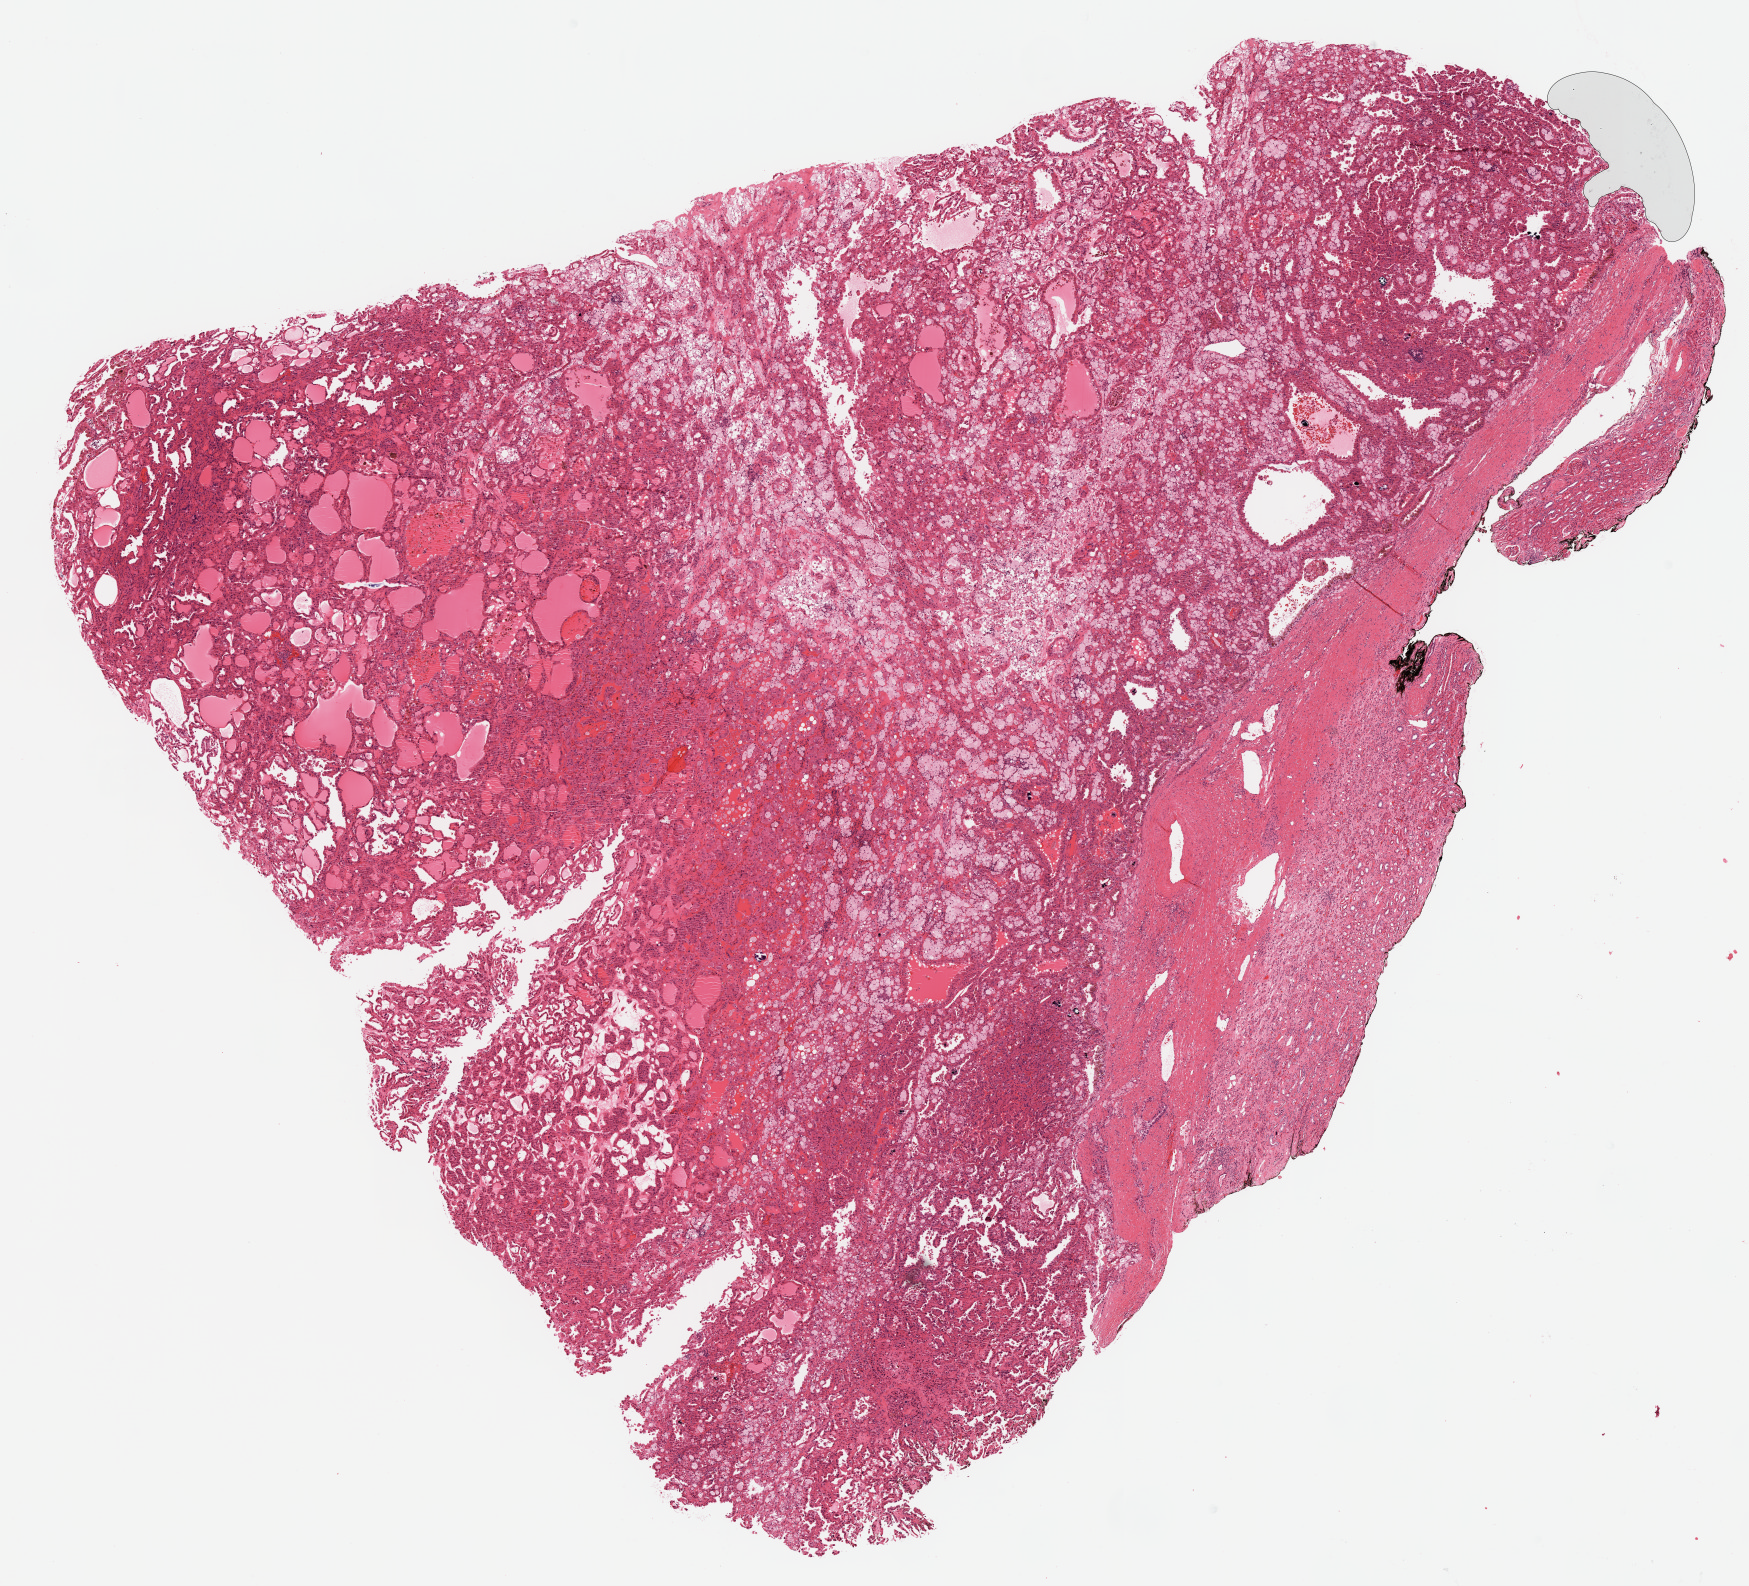
Whole-slide histology image, H&E — shown as a low-resolution overview of the whole scanned area (about 14.0 x 12.7 mm, slide scanned at 20x), FFPE section, kidney, primary tumour sample. Male patient; age at initial diagnosis 58 years.
Histologic diagnosis: Papillary adenocarcinoma, NOS.